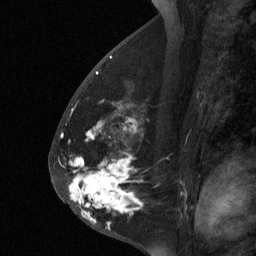
Breast MRI (dynamic contrast-enhanced), one sagittal slice. Position 32 of 64 along the scan axis. Dynamic contrast-enhanced study with each time point stored as its own series, time point 2 of 3 at this slice position (early post-contrast, ordered by acquisition time). 1.5 T. TE 4.8 ms, TR 27 ms. 2 mm slice thickness. 256 × 256 image matrix. Patient: female, 56 years. From the clinical record (not read from this slice): setting: breast cancer imaged before/during neoadjuvant chemotherapy; receptor status: HER2-positive.
Structures marked on this image (semi-automatic segmentation, software-assisted and operator-edited):
- analysis volume of interest (the breast-tissue region the enhancement analysis was run in; not a lesion): bounding box (x1, y1, x2, y2) in pixels: (59, 112, 143, 229)
- tumour enhancement mask (voxels above the 90 % enhancement threshold inside the analysis volume of interest): (69, 163, 140, 222)